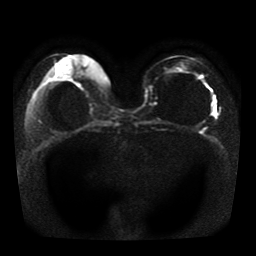
Breast MRI, one axial slice. Position 17 of 41 along the scan axis. Diffusion-weighted series; image 2 of 4 stored at this slice position (different b-values; order by instance number). 1.5 T. 256 × 256 image matrix. Female patient.
Structures marked on this image (outlined manually by an expert reader):
- tumour on diffusion-weighted imaging: bounding box [x1, y1, x2, y2] px = [211, 103, 214, 114]